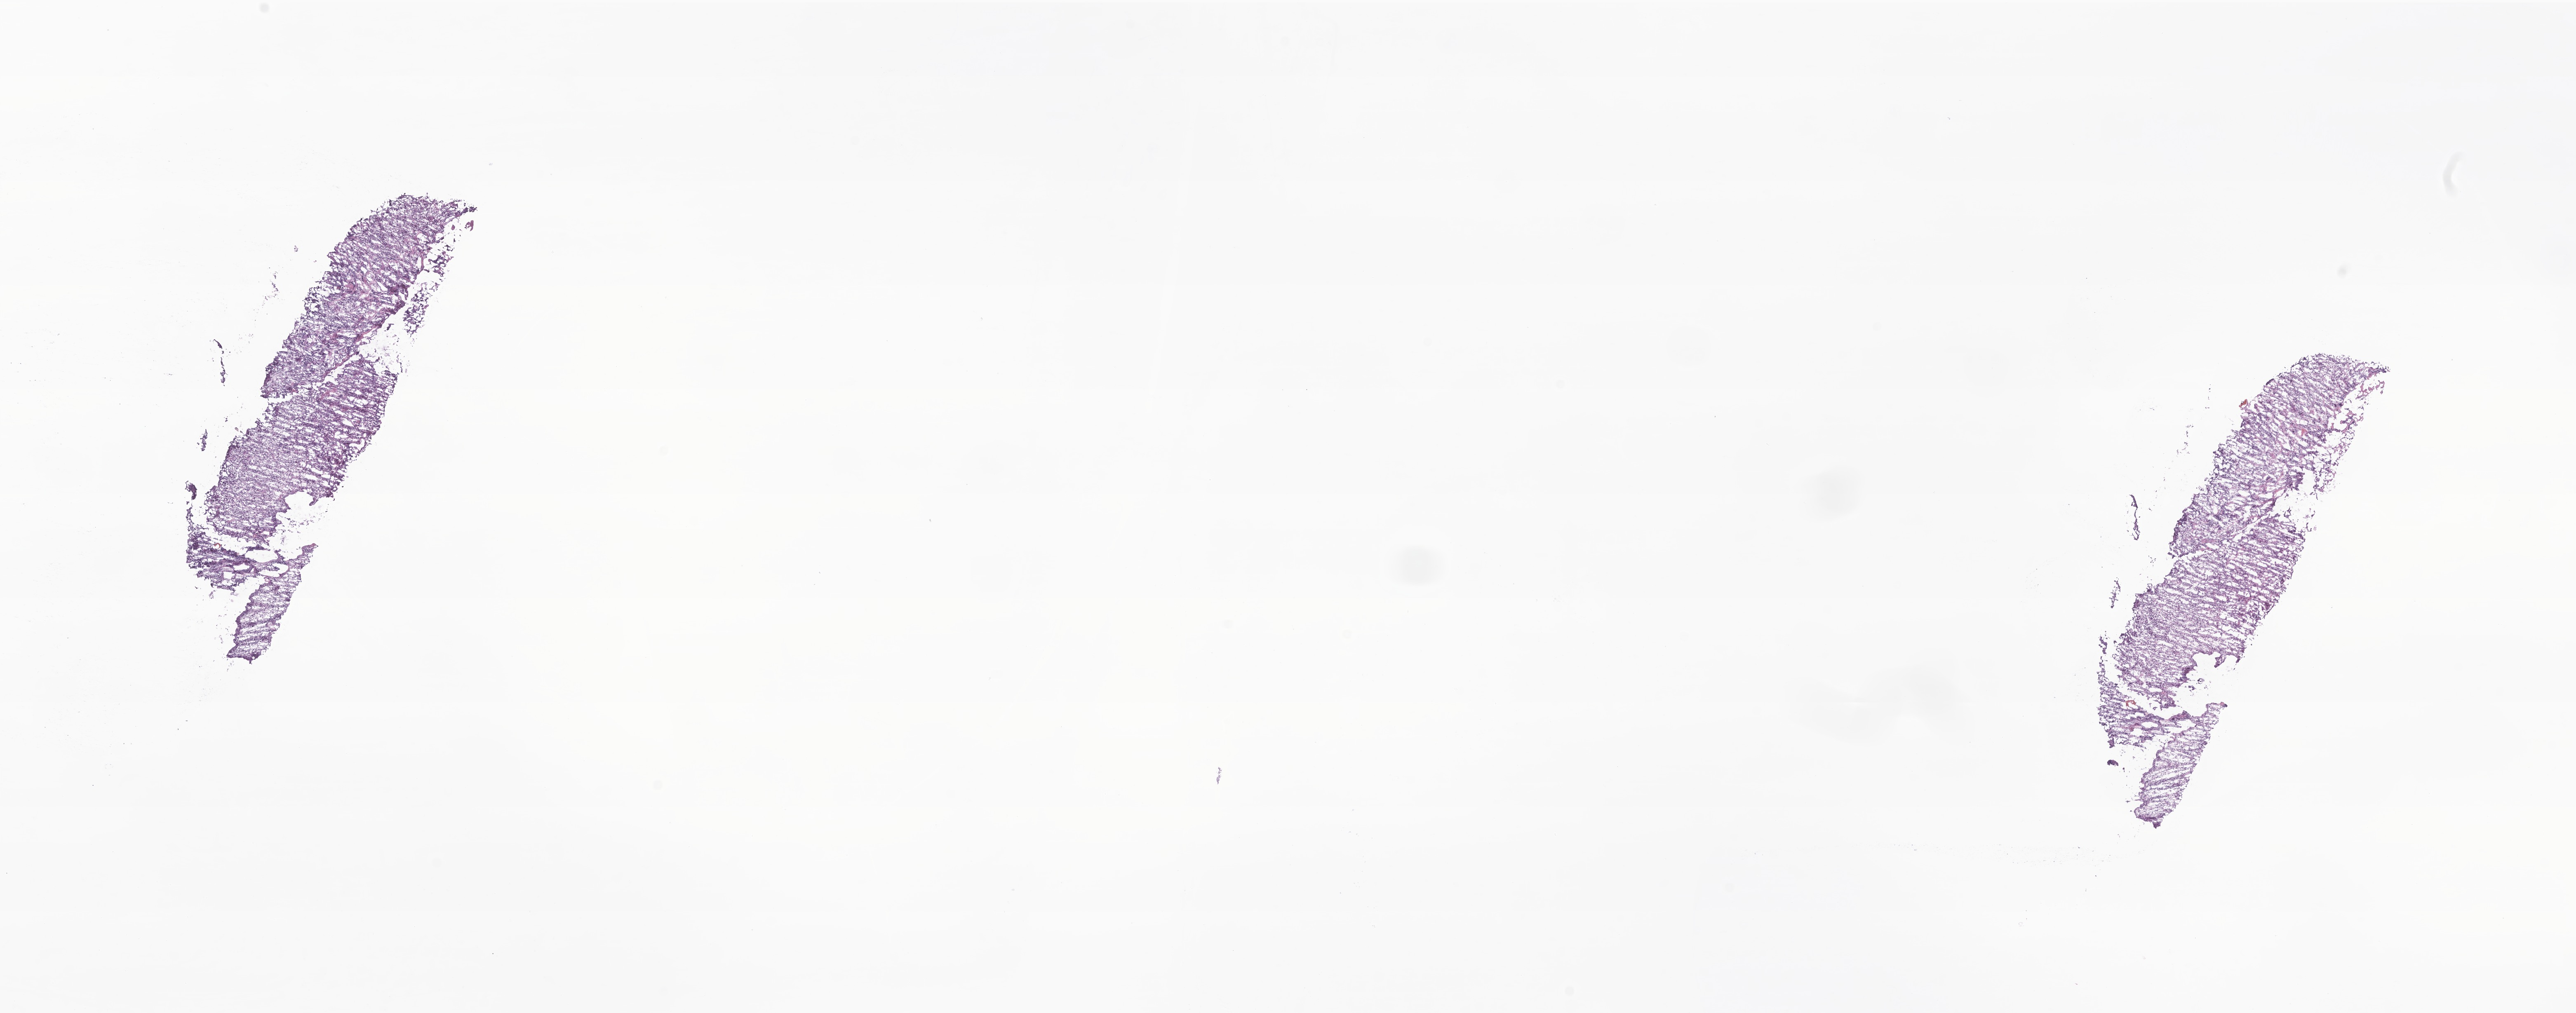
Whole-slide image, hematoxylin and eosin (H&E) stain of tumor tissue from the cerebellum, shown as a low-resolution overview of the whole scanned area (about 26.3 x 10.4 mm); frozen section (OCT-embedded). Female patient, age 113 months (9 years 5 months).
Diagnosis: Medulloblastoma, NOS.